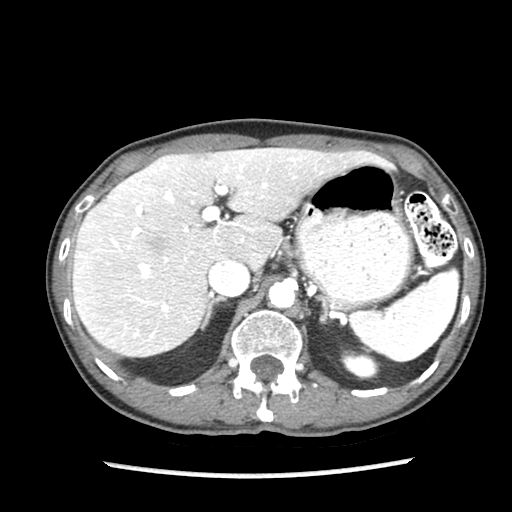
Contrast-enhanced abdominal CT (liver protocol), one axial slice; position 58 of 87 along the scan axis; reconstruction kernel STANDARD; 140 kVp; soft-tissue window (W 400 / L 40 HU); 512 × 512 image matrix, field of view 300 × 300 mm. Case-level facts recorded for this patient, not image findings: diagnosis: hepatocellular carcinoma (patient treated with transarterial chemoembolisation; whether this scan precedes or follows treatment is not stated here); TNM stage (as recorded): Stage-IIIB.
Outlined on this slice (semi-automatically segmented with operator editing):
- liver parenchyma outside the tumour (the mass and vessels are separate outlines, so this box may not span the whole liver): bounding box (x1, y1, x2, y2) in pixels: (72, 148, 372, 356)
- mass: (148, 235, 168, 255)
- liver vessels: (112, 159, 291, 336)